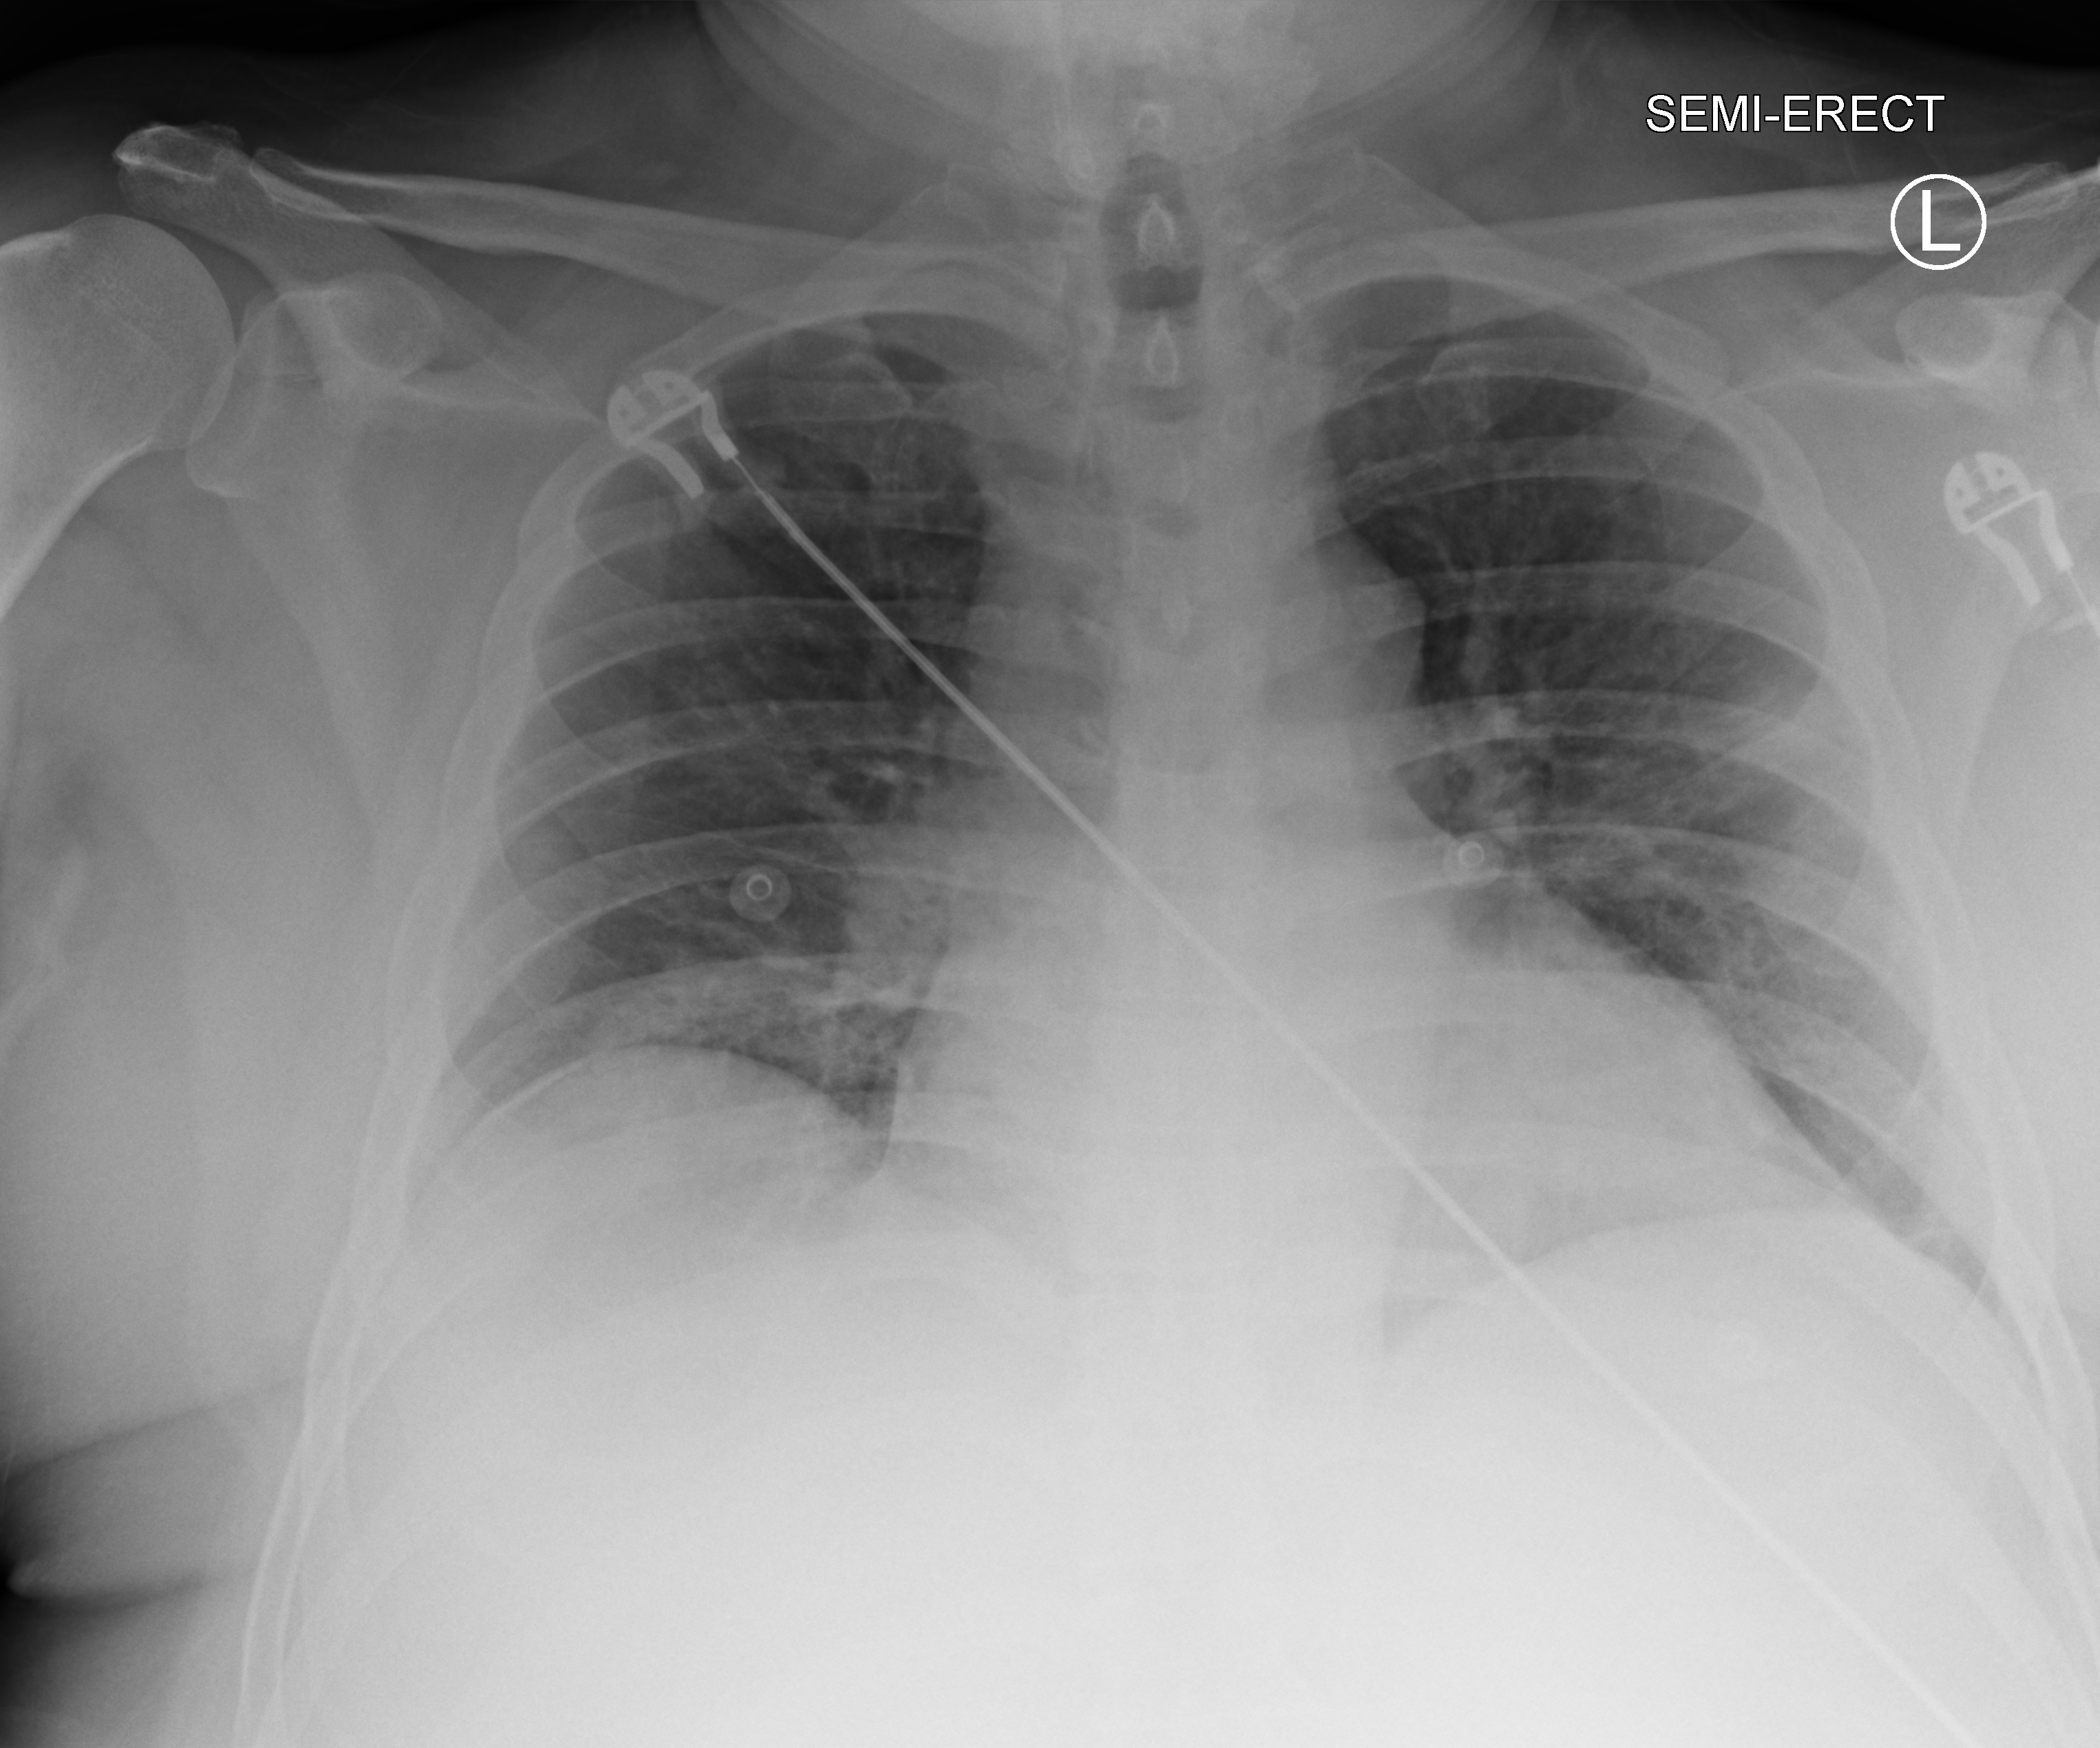
Chest X-ray (portable); anteroposterior (AP) projection. Patient hospitalised with COVID-19; male, aged 60–74 years.
Hospital-stay facts (about this admission, not read from this image; timing relative to this image not recorded): admitted to intensive care during this hospital stay: no; mechanically ventilated during this hospital stay: no.